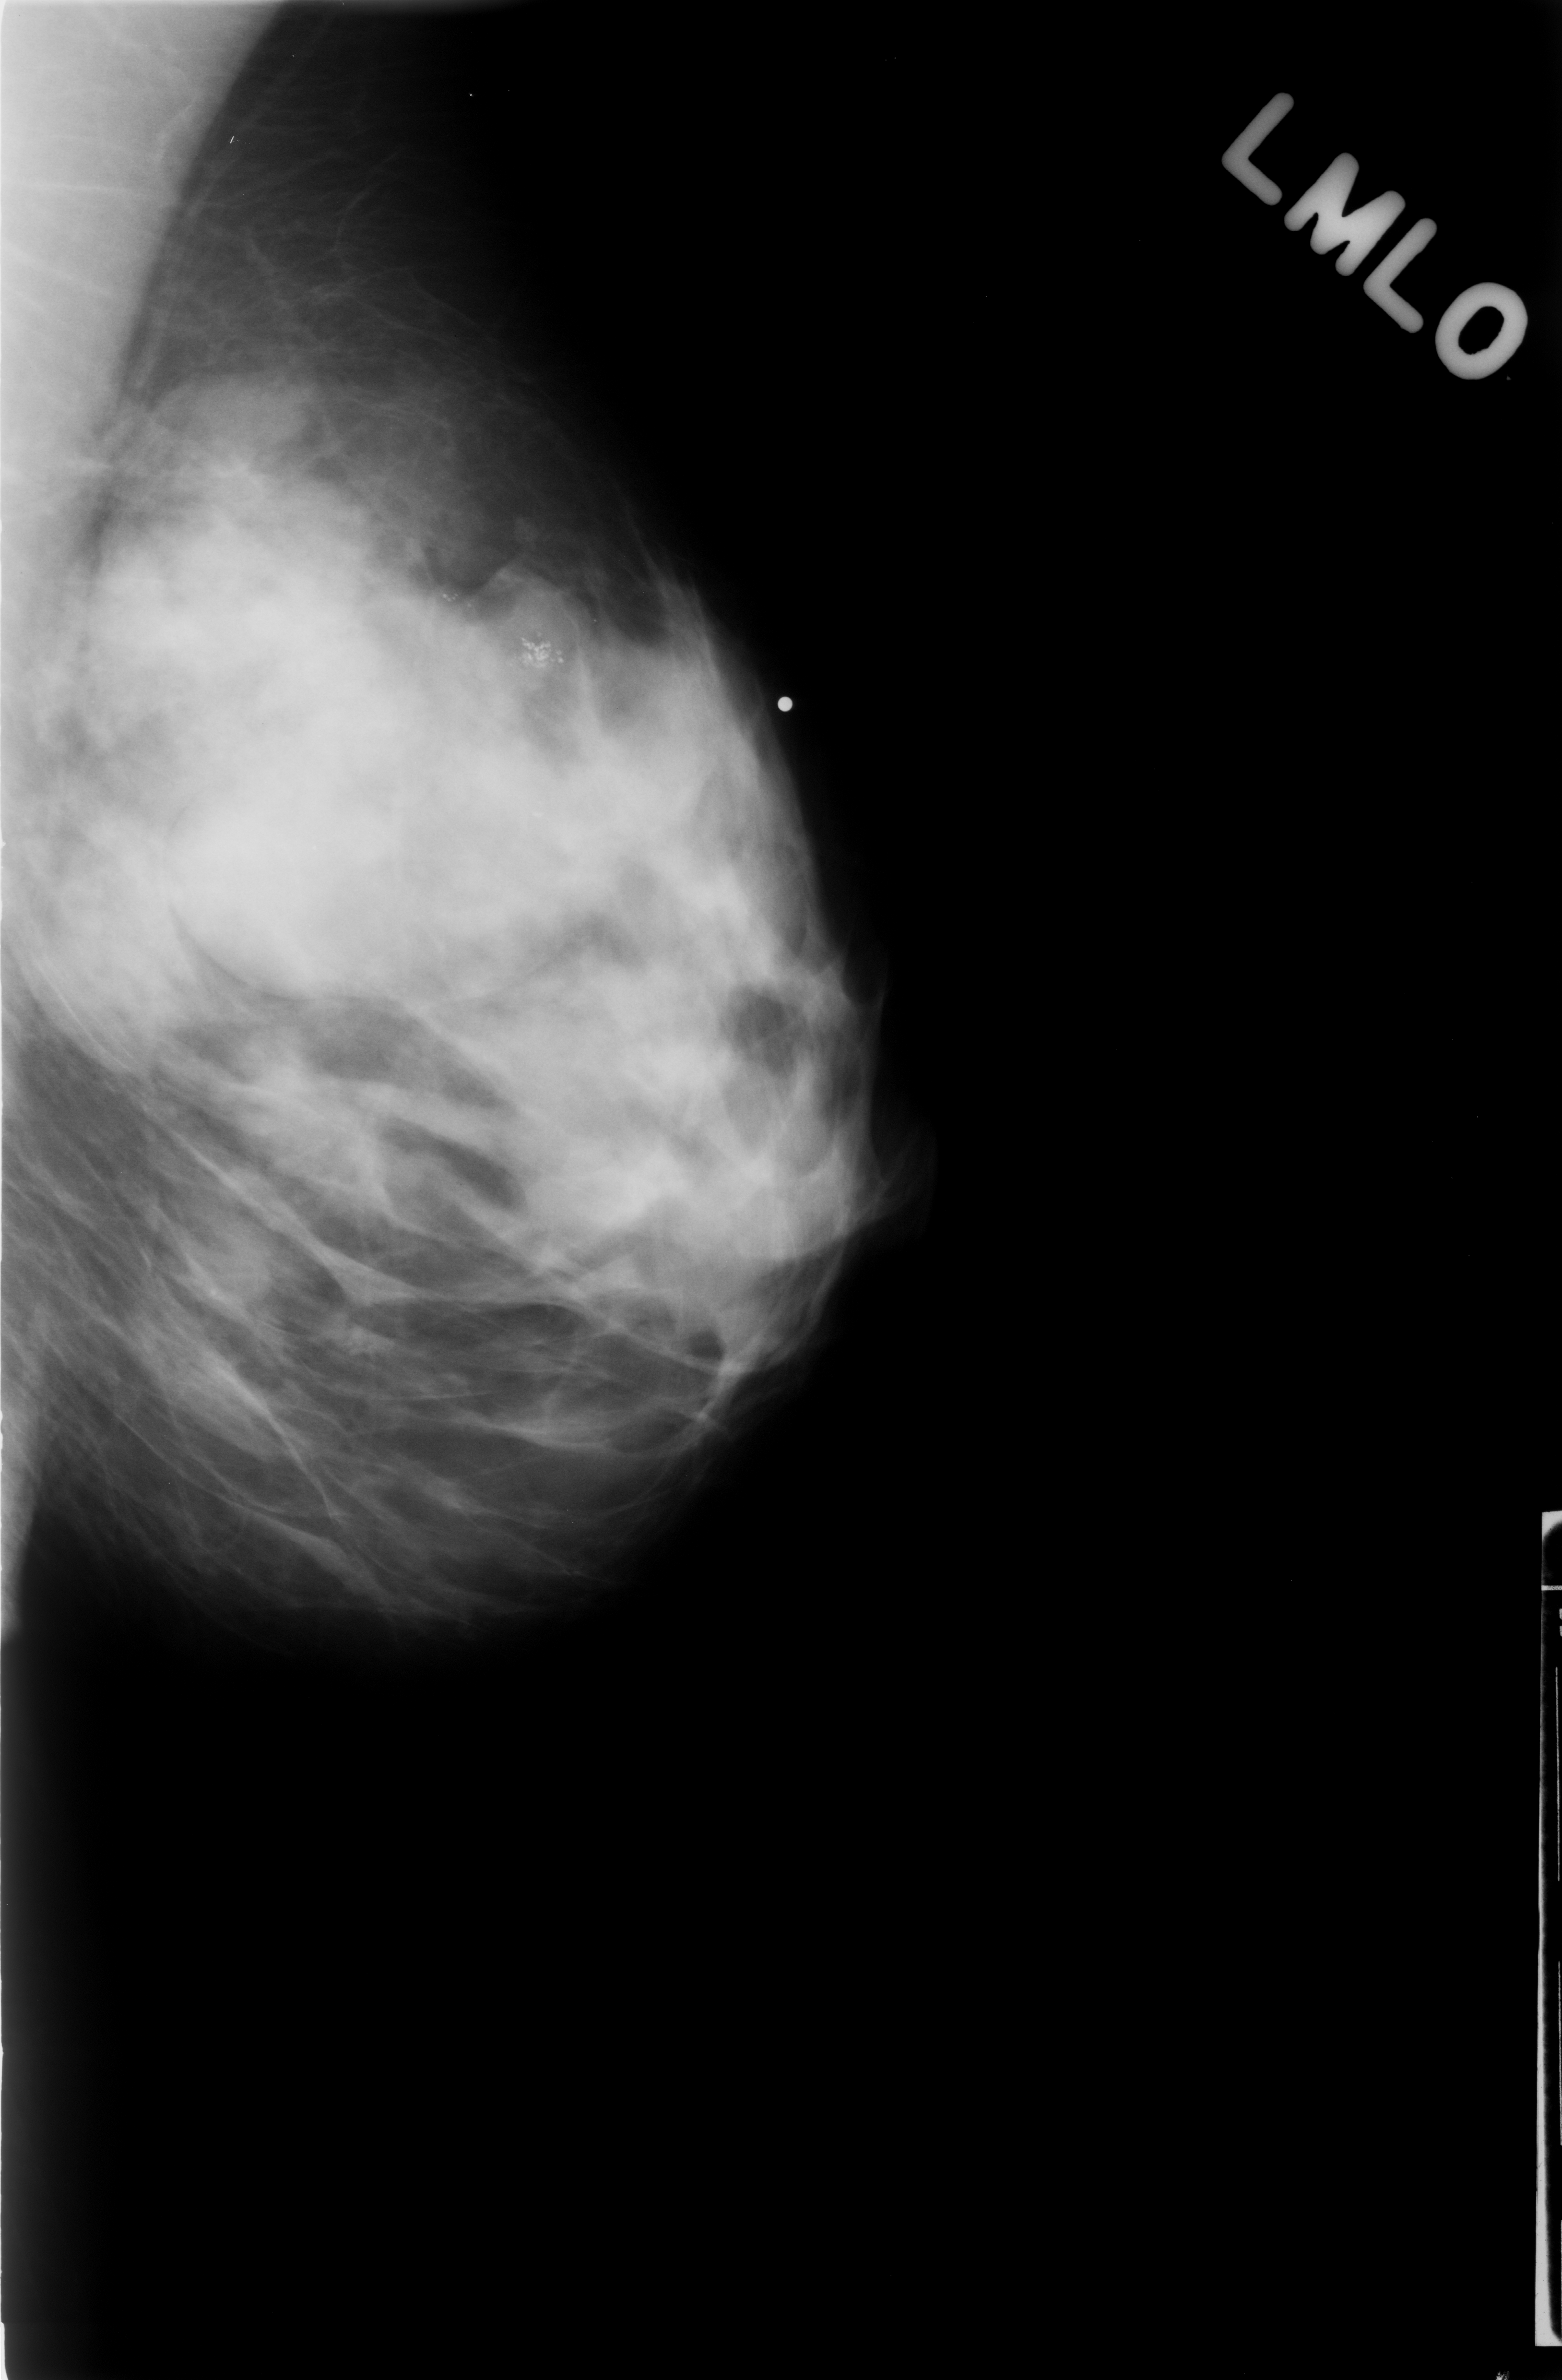
Mammogram (digitized film); left breast; MLO view; breast composition: heterogeneously dense (BI-RADS density category 3 of 4).
Finding: mass, shape oval, margins obscured; BI-RADS assessment category 3; subtlety rating 4 on a 1 (subtle) to 5 (obvious) scale; pathology (as recorded): benign.